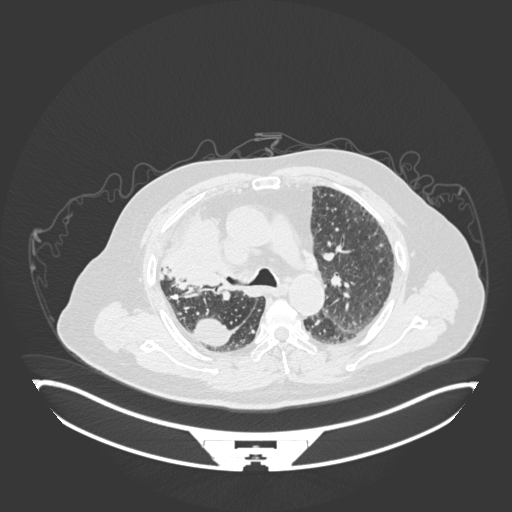
Chest CT, one axial slice; slice 122 of 201 in the series (ordered by position); reconstruction kernel B30f; 120 kVp; lung window (W 1500 / L -600 HU); 1 mm slice thickness; 512 × 512 image matrix, field of view 500 × 500 mm. Male patient, age 69 years. From the clinical record (not read from this slice): clinical TNM (as recorded): T4 N3 M1.
Outlined on this slice (bounding box drawn by a radiologist):
- lung tumour (recorded histology: adenocarcinoma): bounding box <160,209,230,289> (left, top, right, bottom; pixels)